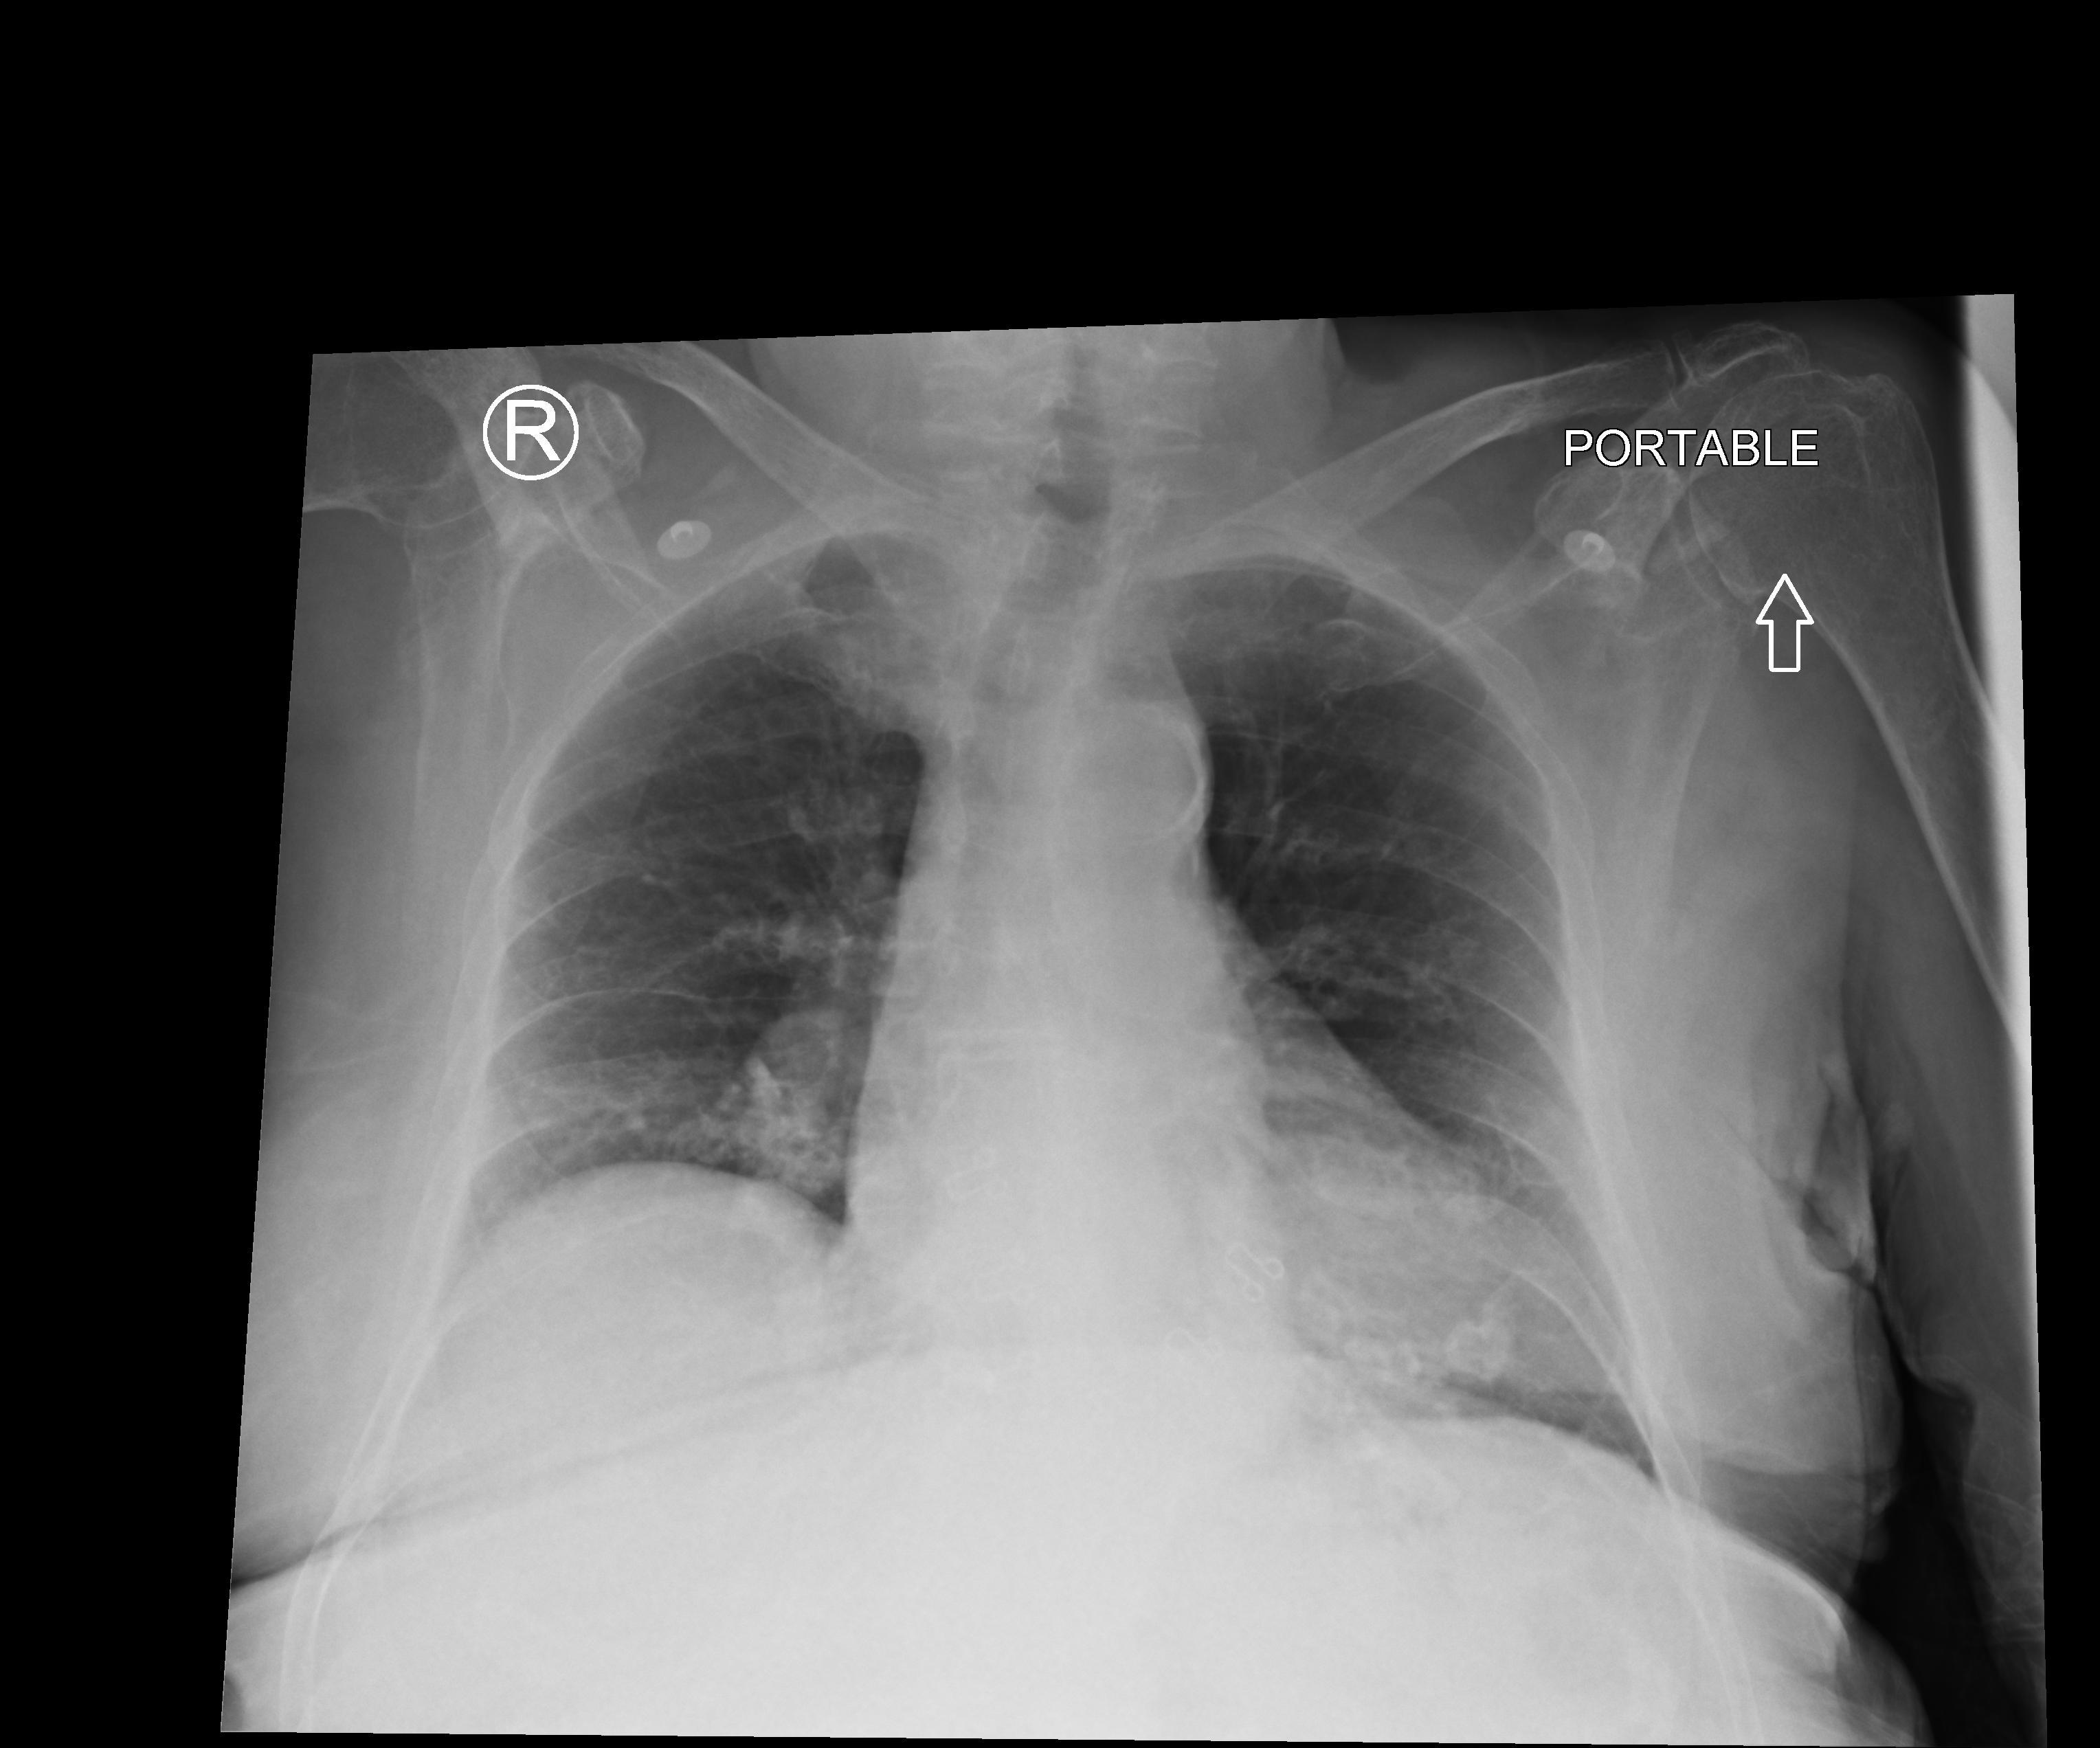
Chest X-ray (portable), anteroposterior (AP) projection. Patient hospitalised with COVID-19; female, aged 75–90 years.
Hospital-stay facts (about this admission, not read from this image; timing relative to this image not recorded): chronic kidney disease (admission record): no.